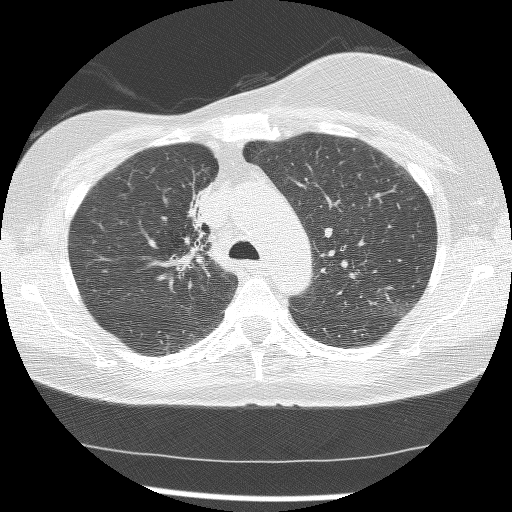
Low-dose screening chest CT, axial slice; first (baseline) screen; lung window (W 1500 / L -600 HU); 2.5 mm slice thickness; lung (sharp) reconstruction kernel (BONE); slice 46 of 172 in the series; 512 × 512 image matrix. Female participant, aged 56 years at enrolment. Current smoker at enrolment.
Expert reader's lesion annotation, bounding box [x1, y1, x2, y2] px = [164, 178, 221, 268]. The screening reader recorded 2 non-calcified nodules or masses ≥4 mm on this exam (right lower lobe, right middle lobe); which of them this box marks is not recorded. Official screen result: positive, change unspecified: nodule(s) >= 4 mm or enlarging nodule(s), mass(es), or other non-specific abnormalities suspicious for lung cancer. Participant outcome: lung cancer diagnosed 1185 days after this screen — adenocarcinoma, NOS, right upper lobe, stage IIIB (AJCC 6th edition), 8 mm at pathology.